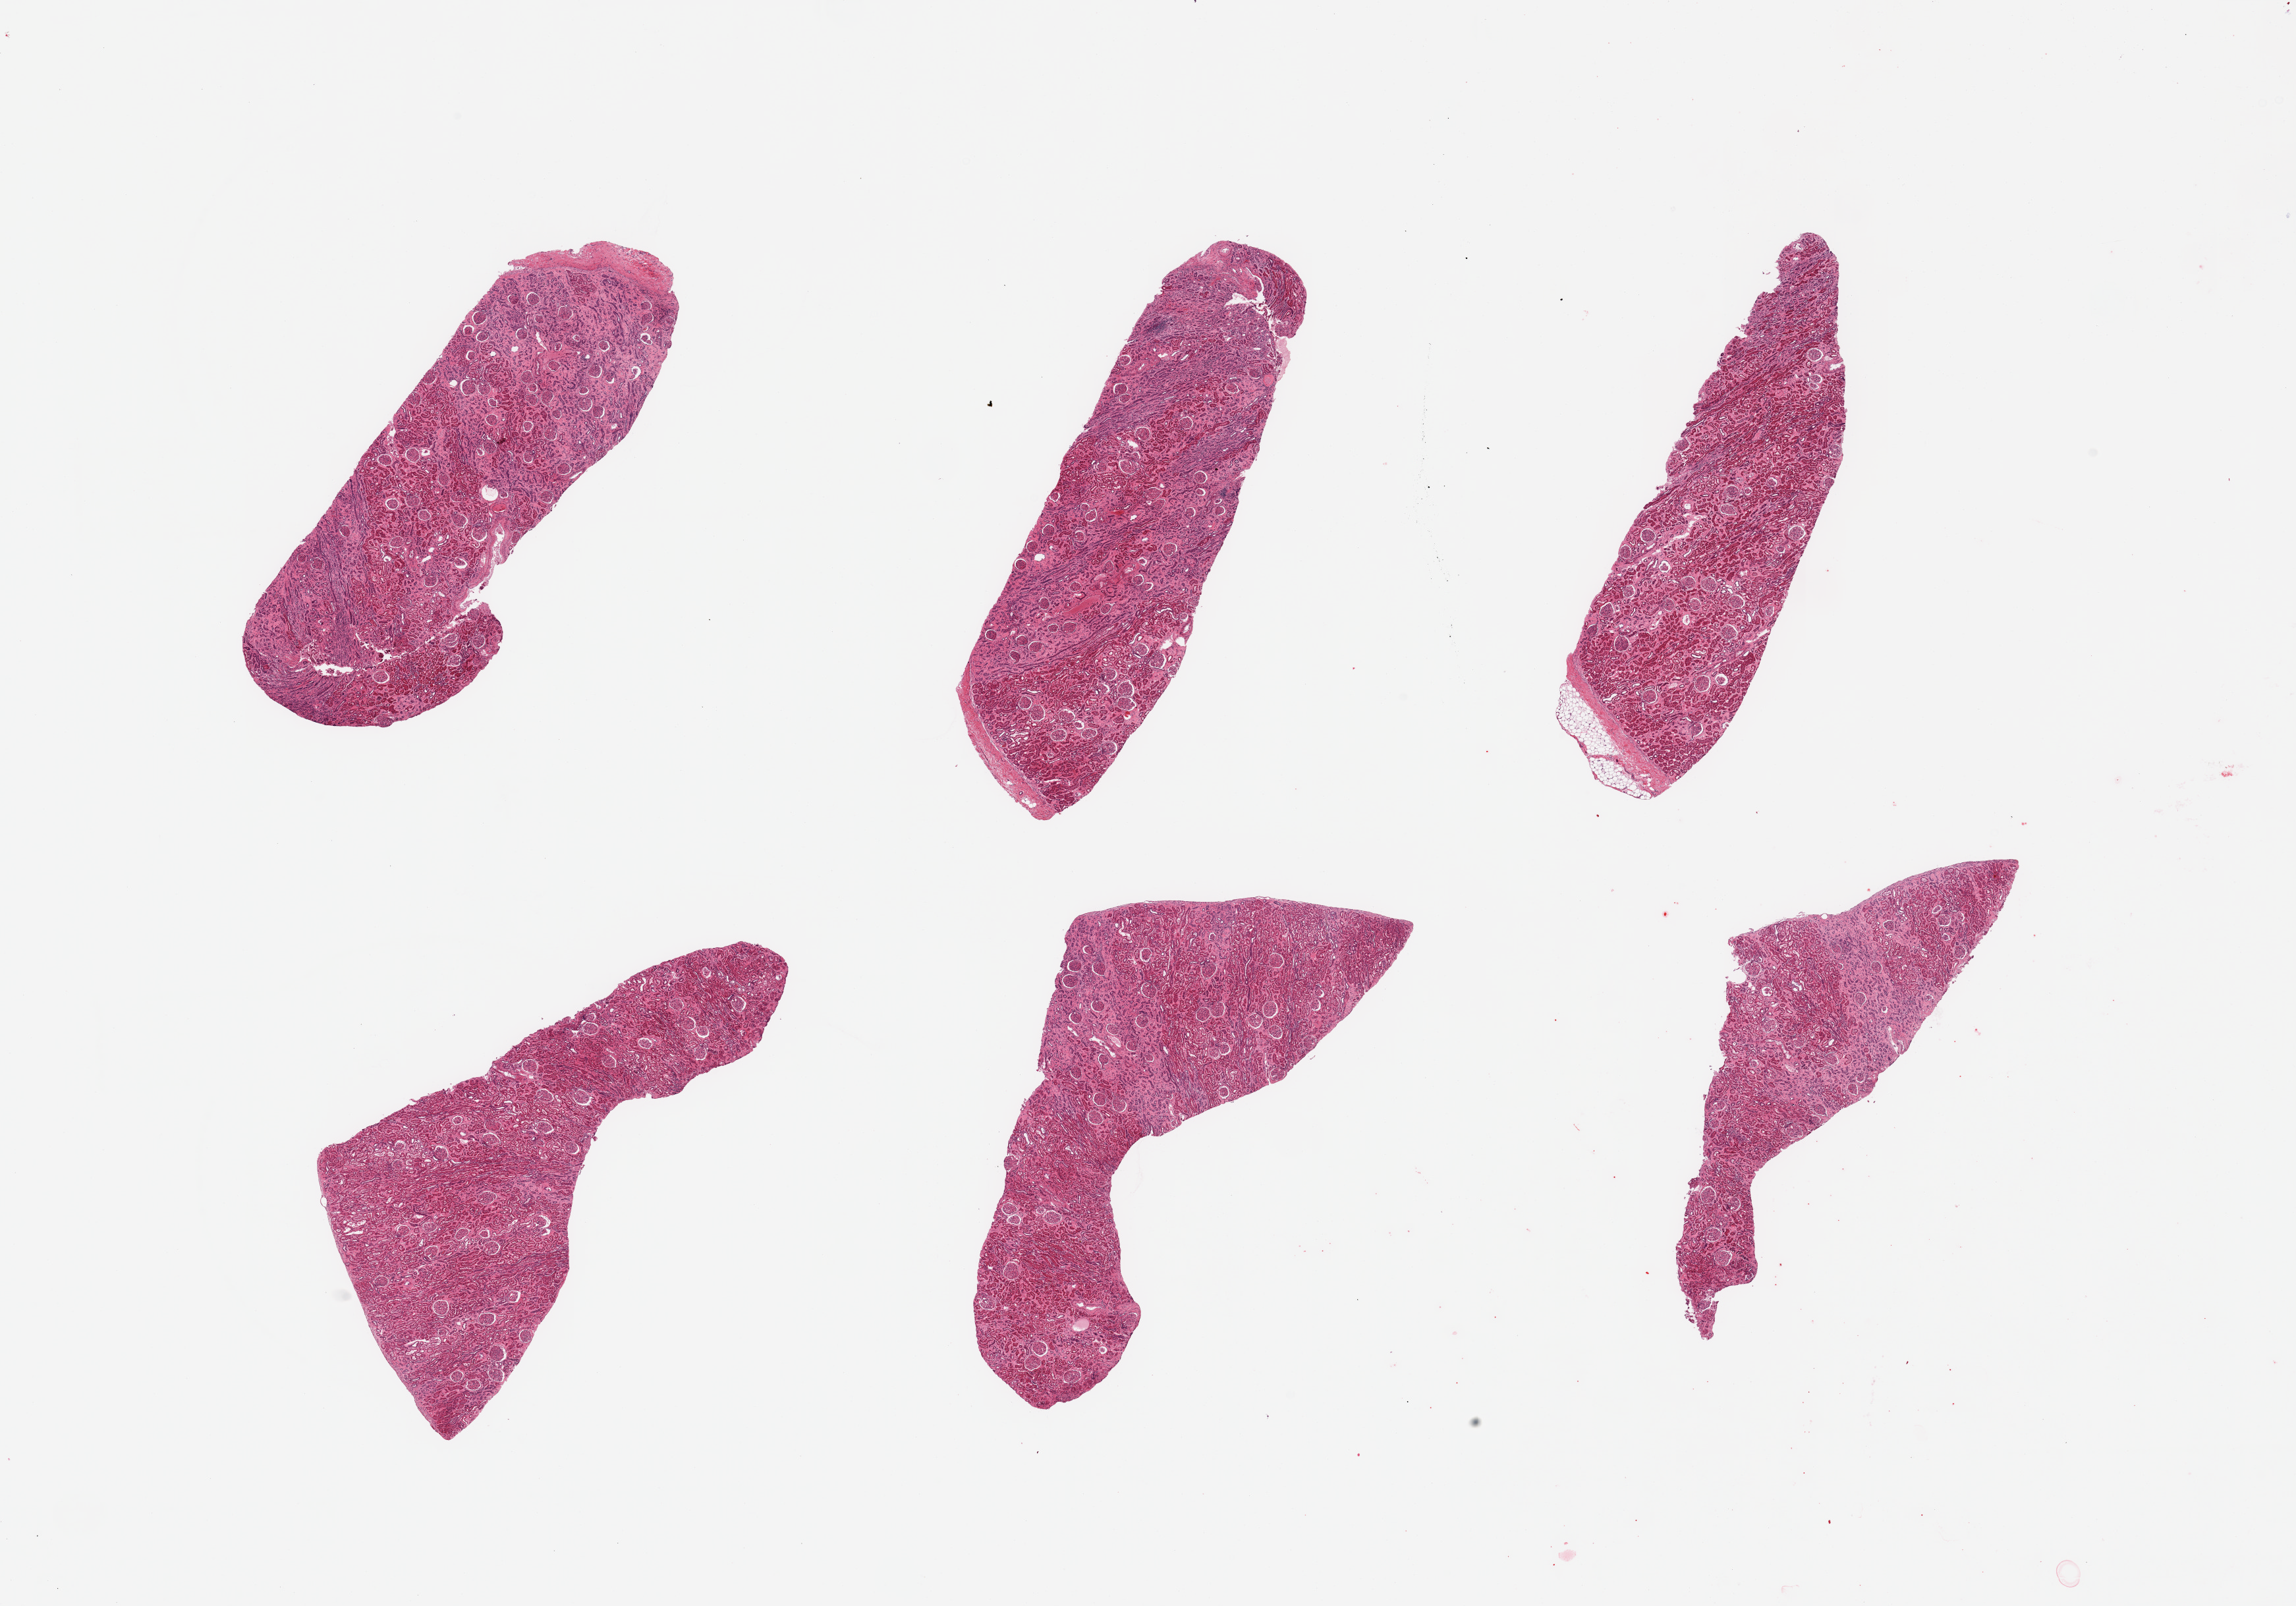
H&E whole-slide image — shown as a low-resolution overview of the whole scanned area (about 27.6 x 19.3 mm, slide scanned at 20x); PAXgene-fixed, paraffin-embedded tissue; section of renal cortex (target tissue); tissue donor sample. Male donor.
Review note (as recorded): 6 pieces; patchy interstitial fibrosis, but no glomerular or vascular lesions.